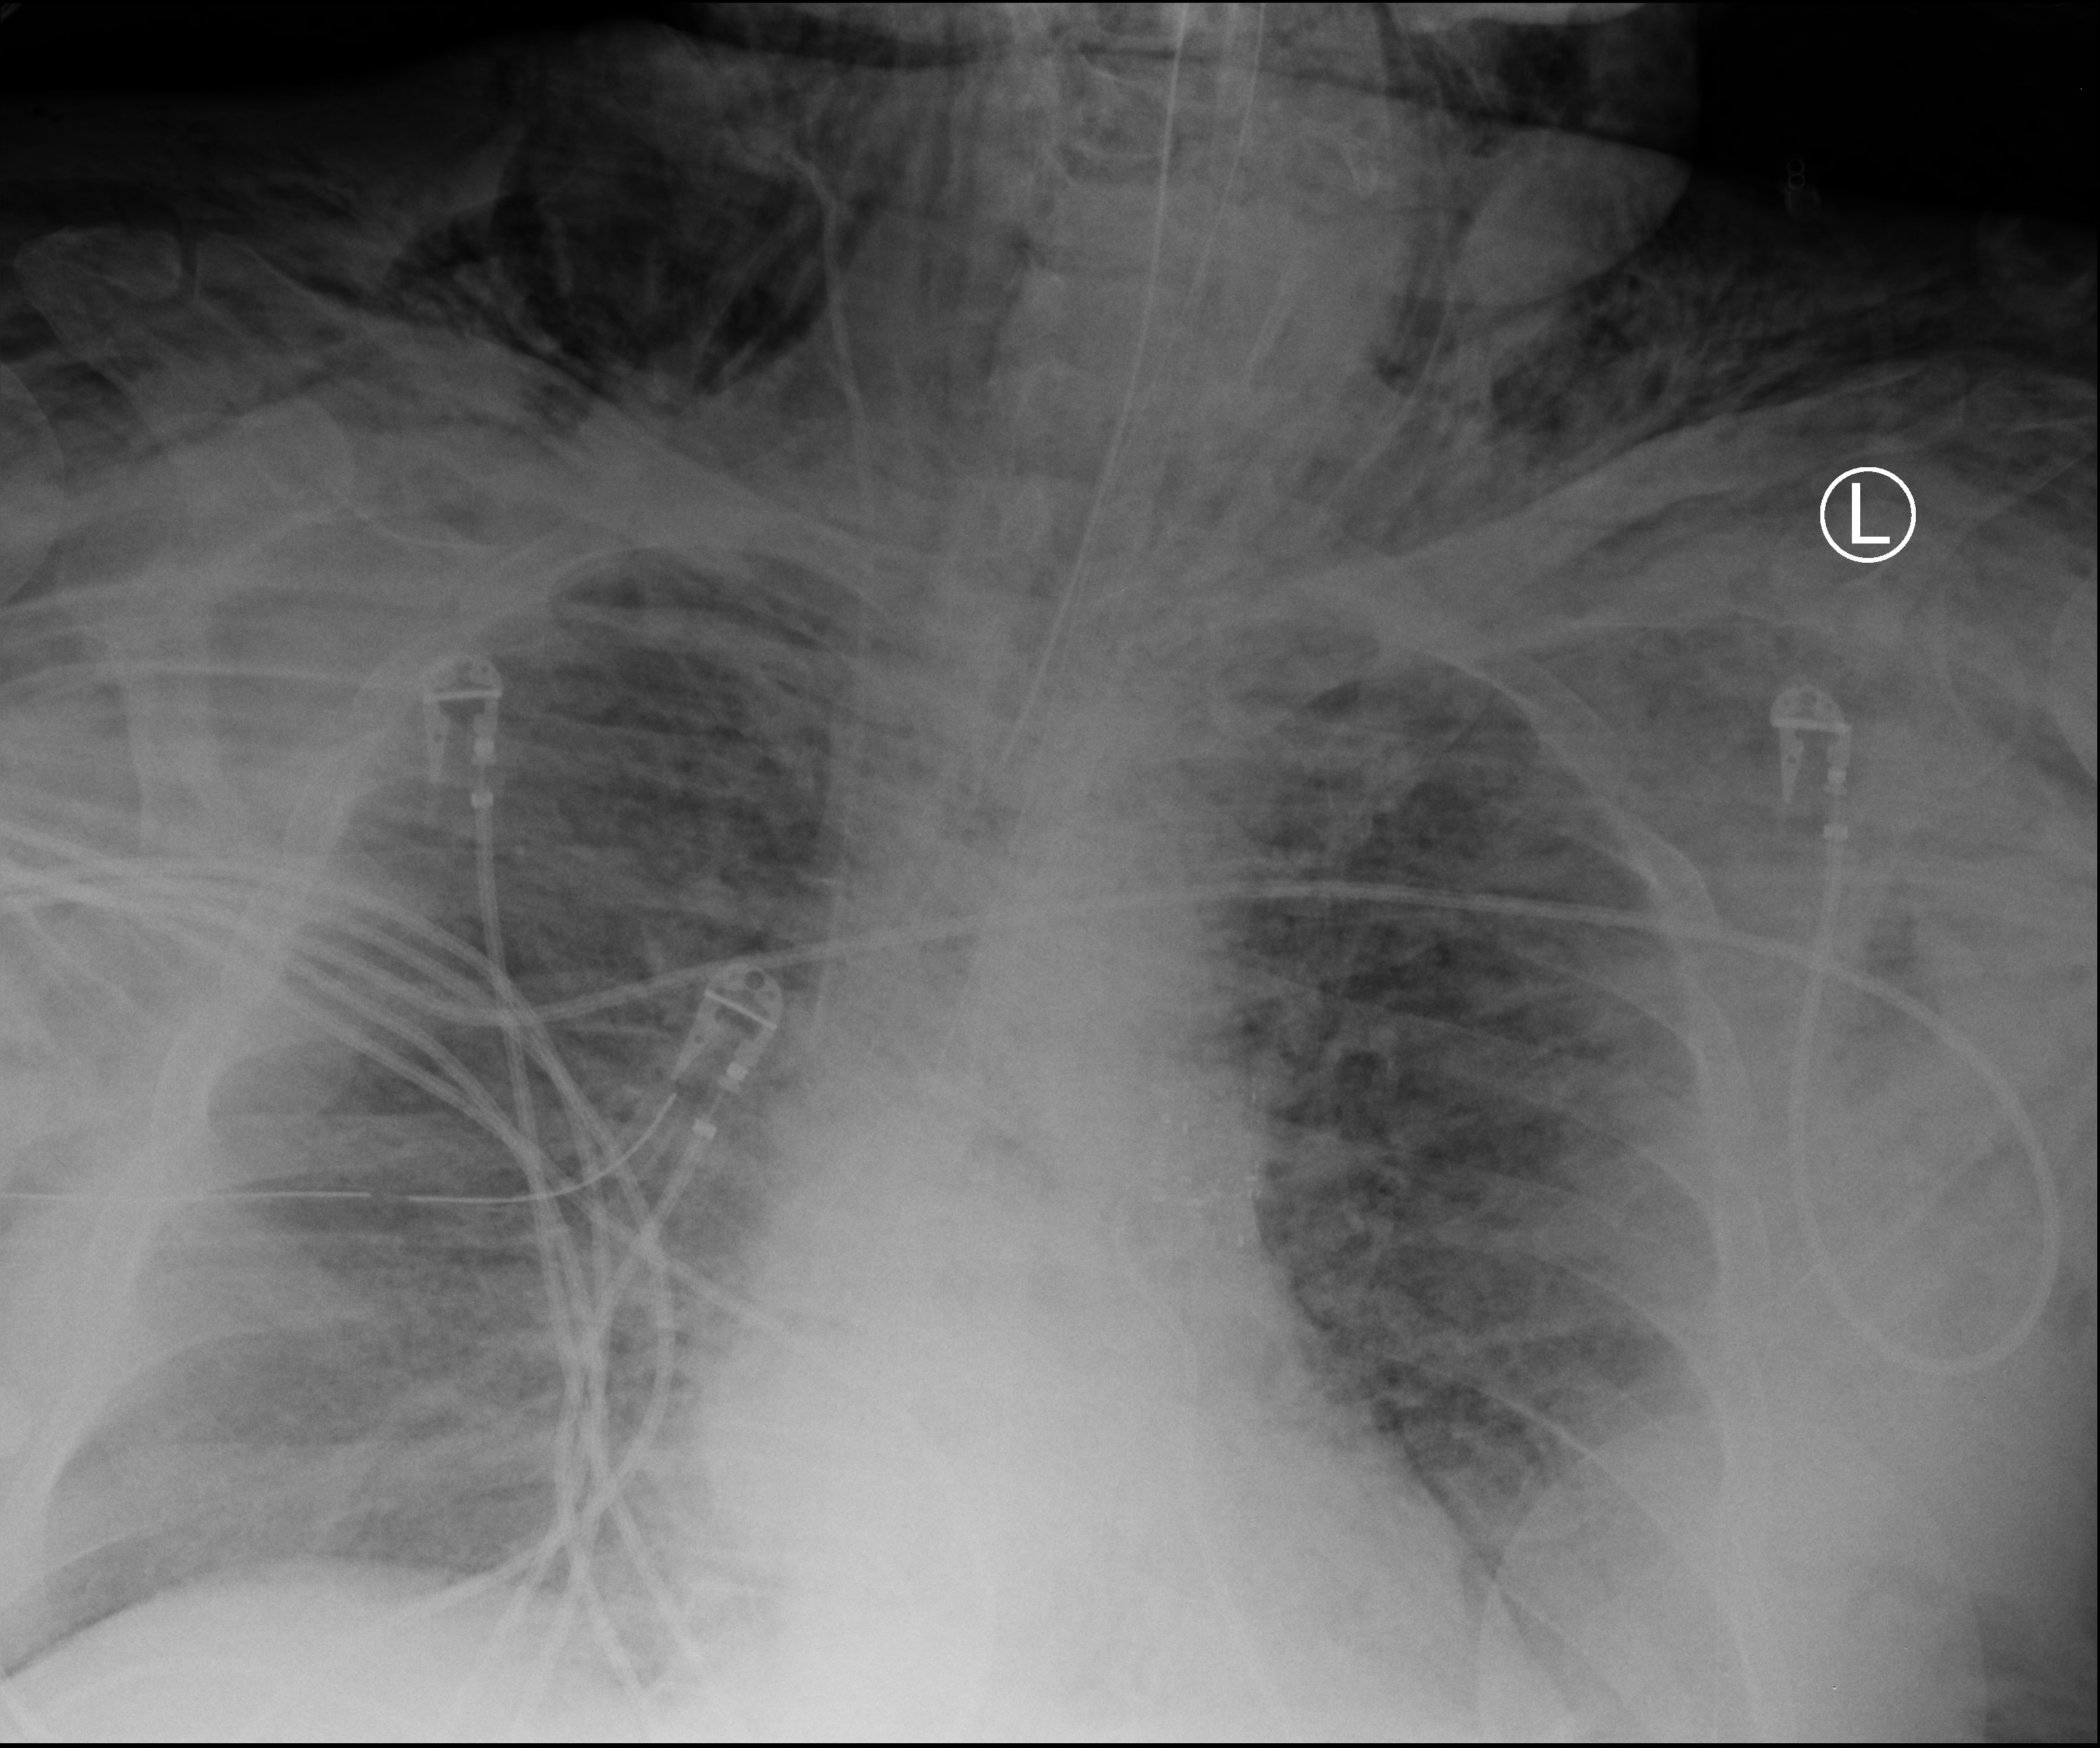
Portable chest radiograph; anteroposterior (AP) projection. Patient hospitalised with COVID-19, aged 18–59 years.
Hospital-stay facts (about this admission, not read from this image; timing relative to this image not recorded):
- COPD (admission record): no